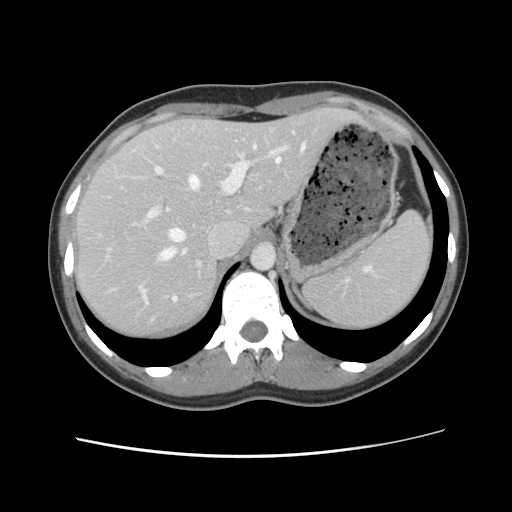
Contrast-enhanced abdominal CT, one axial slice. Slice 83 of 134 in the series (ordered by position). Intravenous contrast given. Soft-tissue window (W 400 / L 40 HU). 512 × 512 image matrix, field of view 339 × 339 mm. Female patient, age 33 years. From the clinical record (not read from this slice): diagnosis: colorectal cancer liver metastases, imaged before liver resection; multiple liver metastases: yes; largest metastasis: 4.5 cm.
Outlined on this slice (outlined manually by an expert reader):
- hepatic veins: bounding box <140,144,306,302> (left, top, right, bottom; pixels)
- liver: <75,108,356,339>
- planned liver remnant (the part of the liver to remain after resection): <75,108,355,339>
- portal vein (with intrahepatic branches): <147,139,290,219>